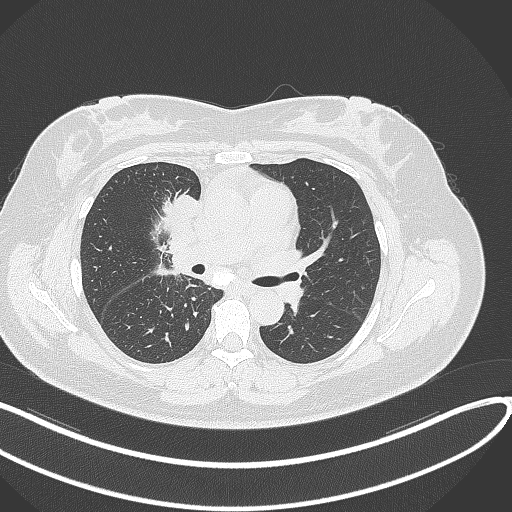
Chest CT, one axial slice. Slice 156 of 303 in the series (ordered by position). Lung window (W 1500 / L -600 HU). 1 mm slice thickness. 512 × 512 image matrix. Female patient, age 46 years. From the clinical record (not read from this slice): clinical TNM (as recorded): T2a N1 M0.
Annotated regions visible in this slice (rectangle marked by the reading radiologist):
- lung tumour (recorded histology: adenocarcinoma): bounding box [x1, y1, x2, y2] px = [167, 185, 200, 221]